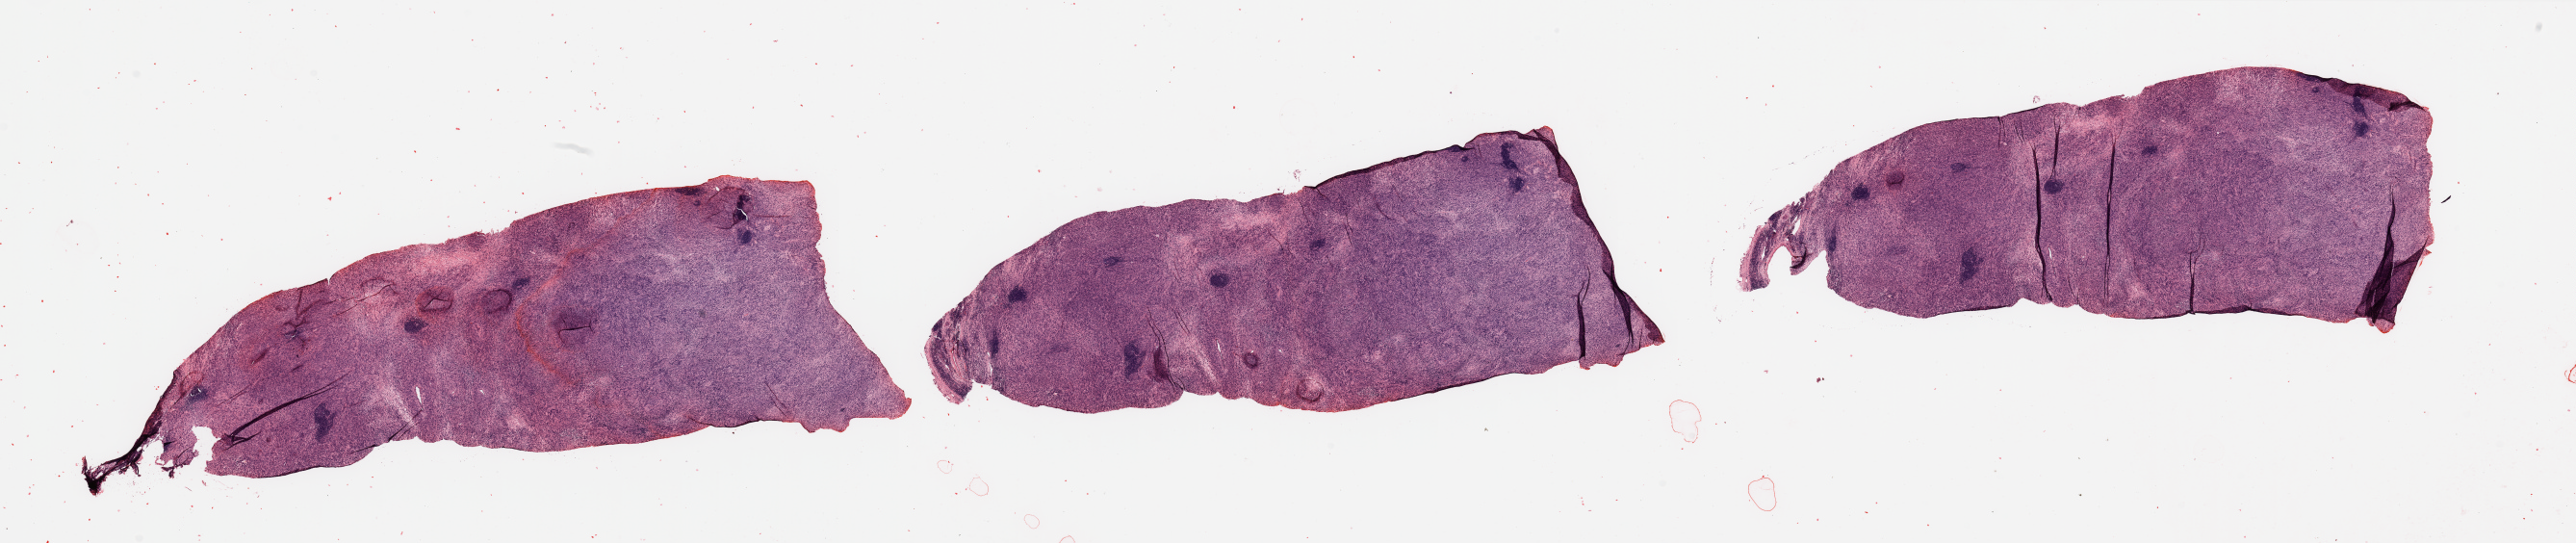
Digitized H&E tissue section (whole slide) — low-resolution overview of the scanned area, about 42.3 x 8.9 mm (acquisition: 20x scan); tumour tissue sample, sampled site: lymph node. 58-year-old female patient.
Patient diagnosis: Malignant melanoma, NOS.